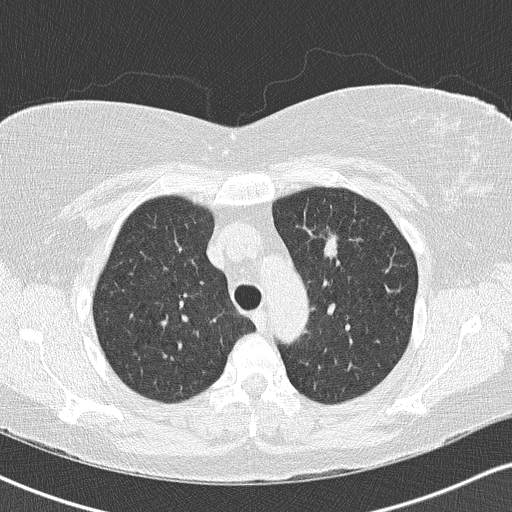
Low-dose screening chest CT, one axial slice; position 112 of 146 along the scan axis; reconstruction kernel B50f; 120 kVp; lung window (W 1500 / L -600 HU); 512 × 512 image matrix, field of view 328 × 328 mm.
Structures marked on this image (manually delineated by an expert):
- lesion 1 (tumor, upper lobe of left lung): box from (x=324, y=232) to (x=338, y=260) px